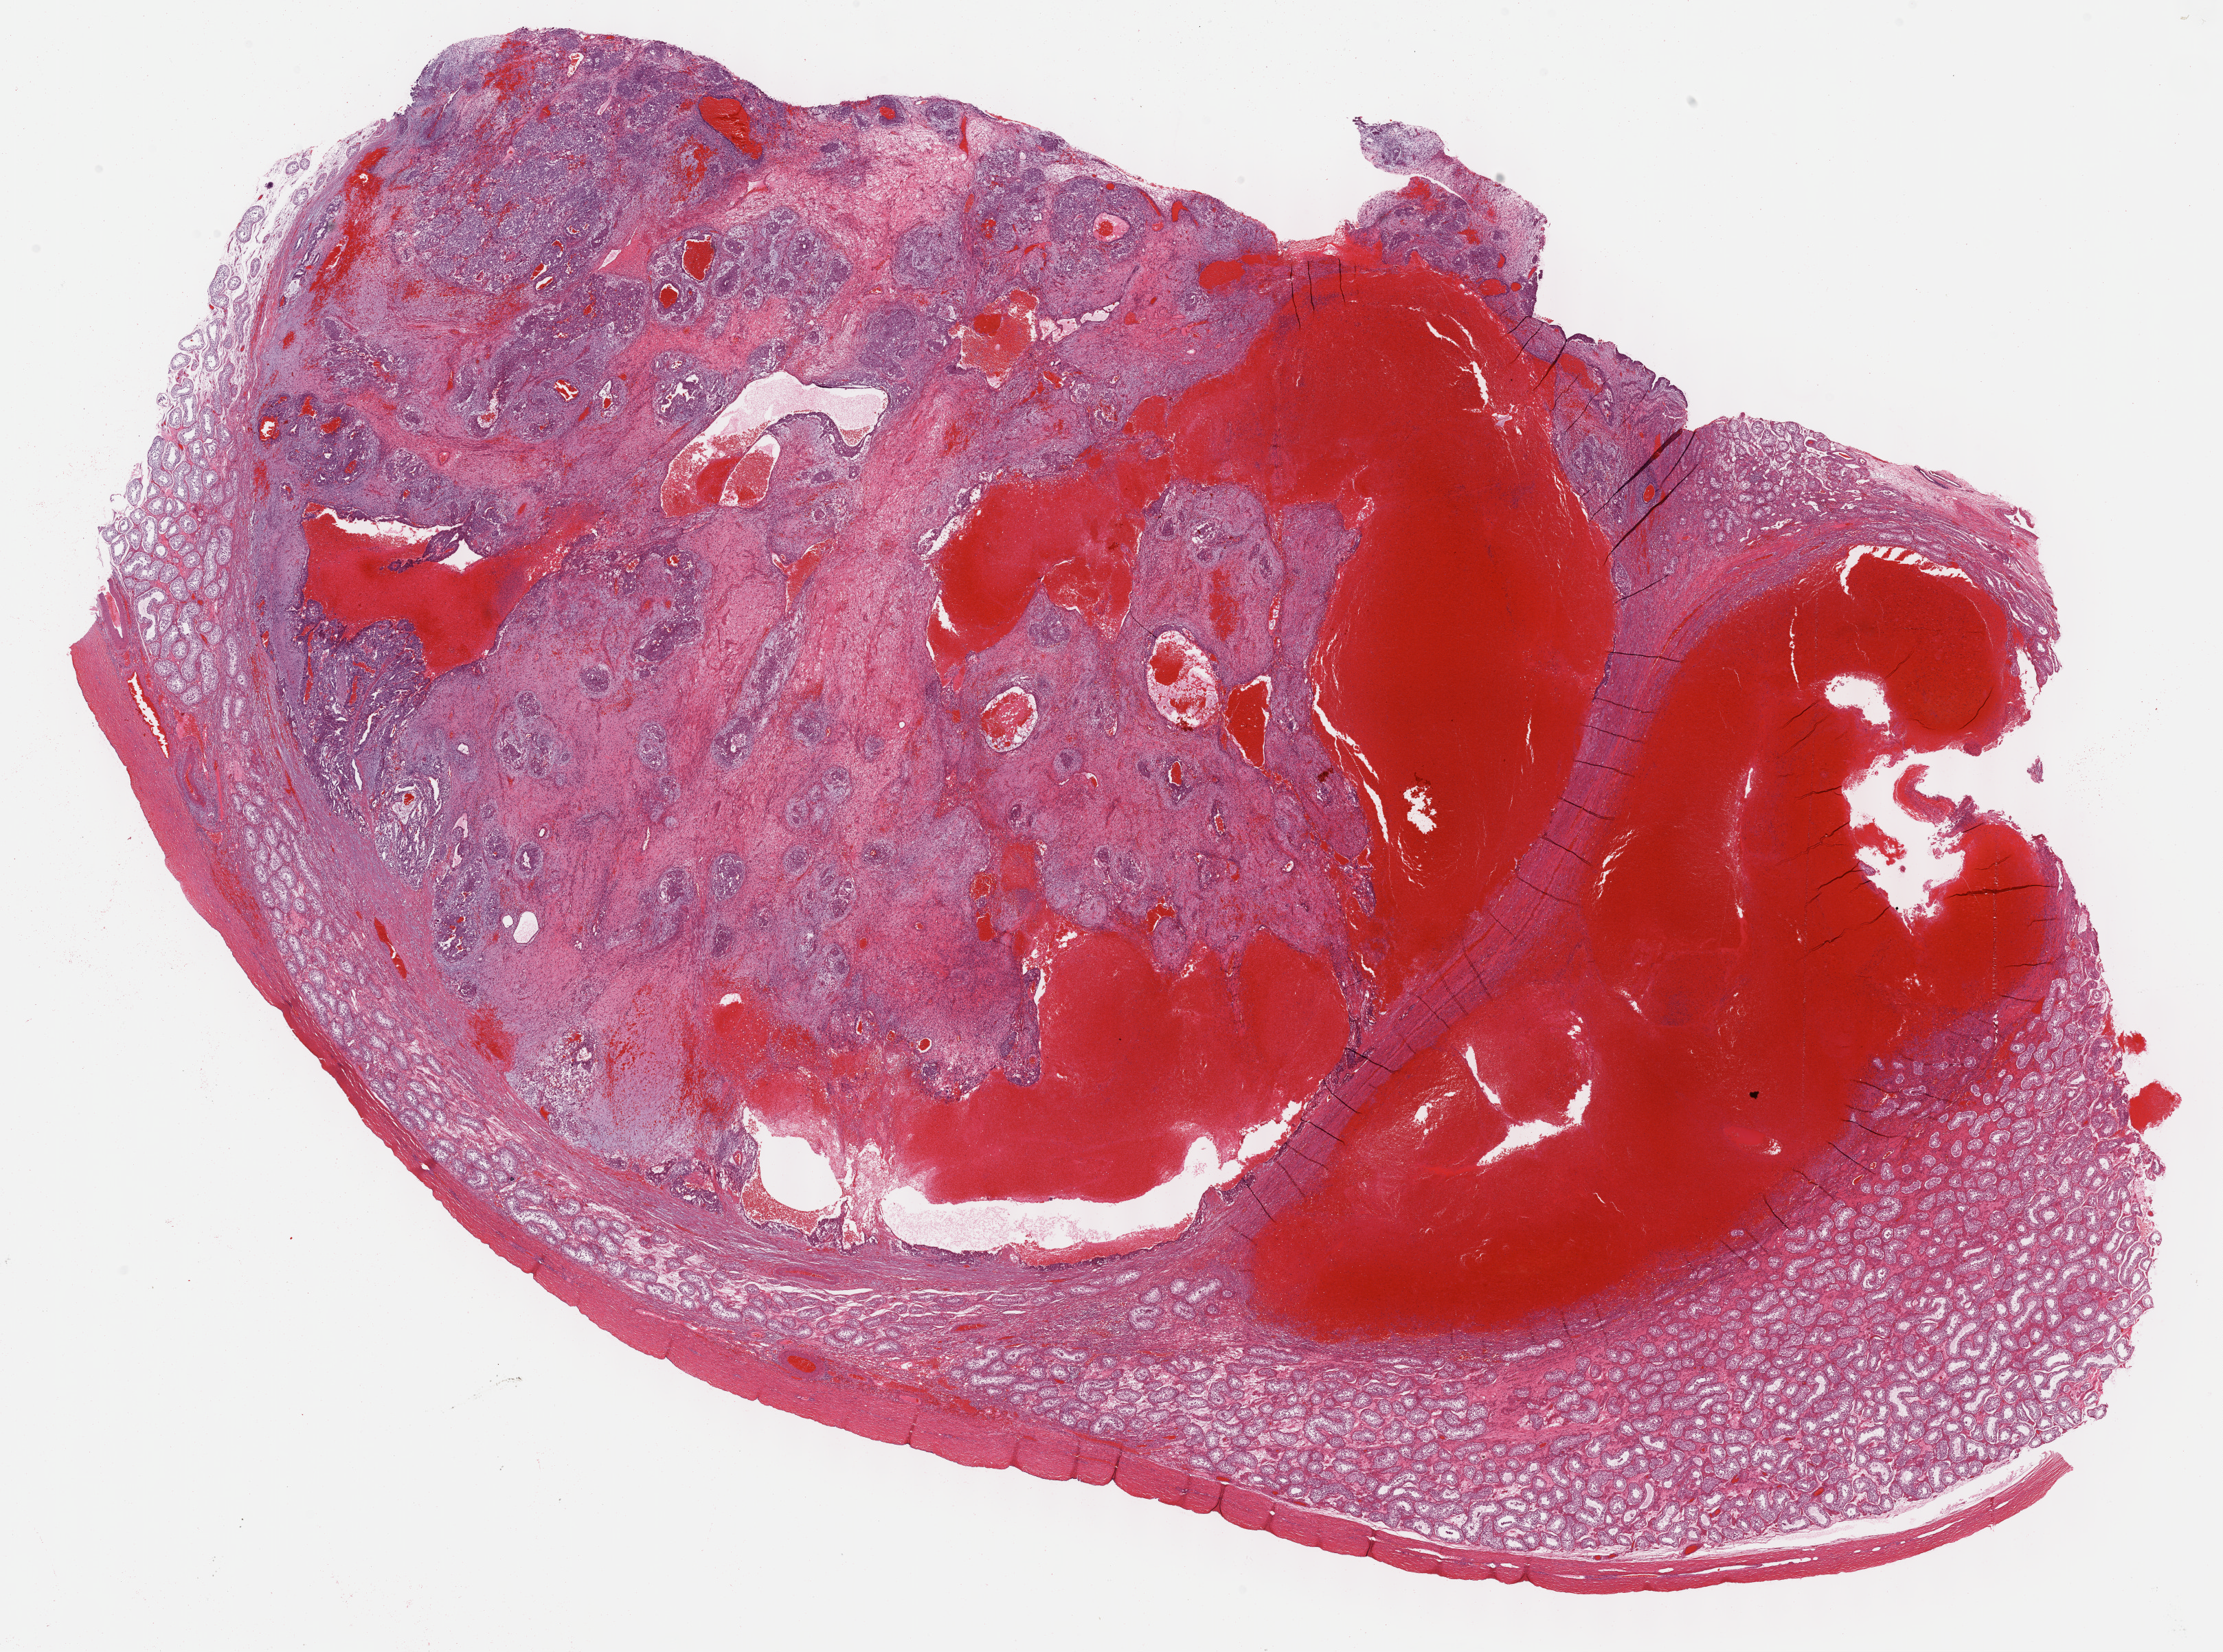
Digitized H&E tissue section (whole slide) — shown as a low-resolution overview of the whole scanned area (about 26.2 x 19.5 mm, slide scanned at 40x), formalin-fixed paraffin-embedded (FFPE) diagnostic section, sample: primary tumour, testis. Patient: male, age at initial diagnosis 24 years.
- histologic diagnosis: Embryonal carcinoma, NOS
- AJCC pathologic stage: IS (7th edition)